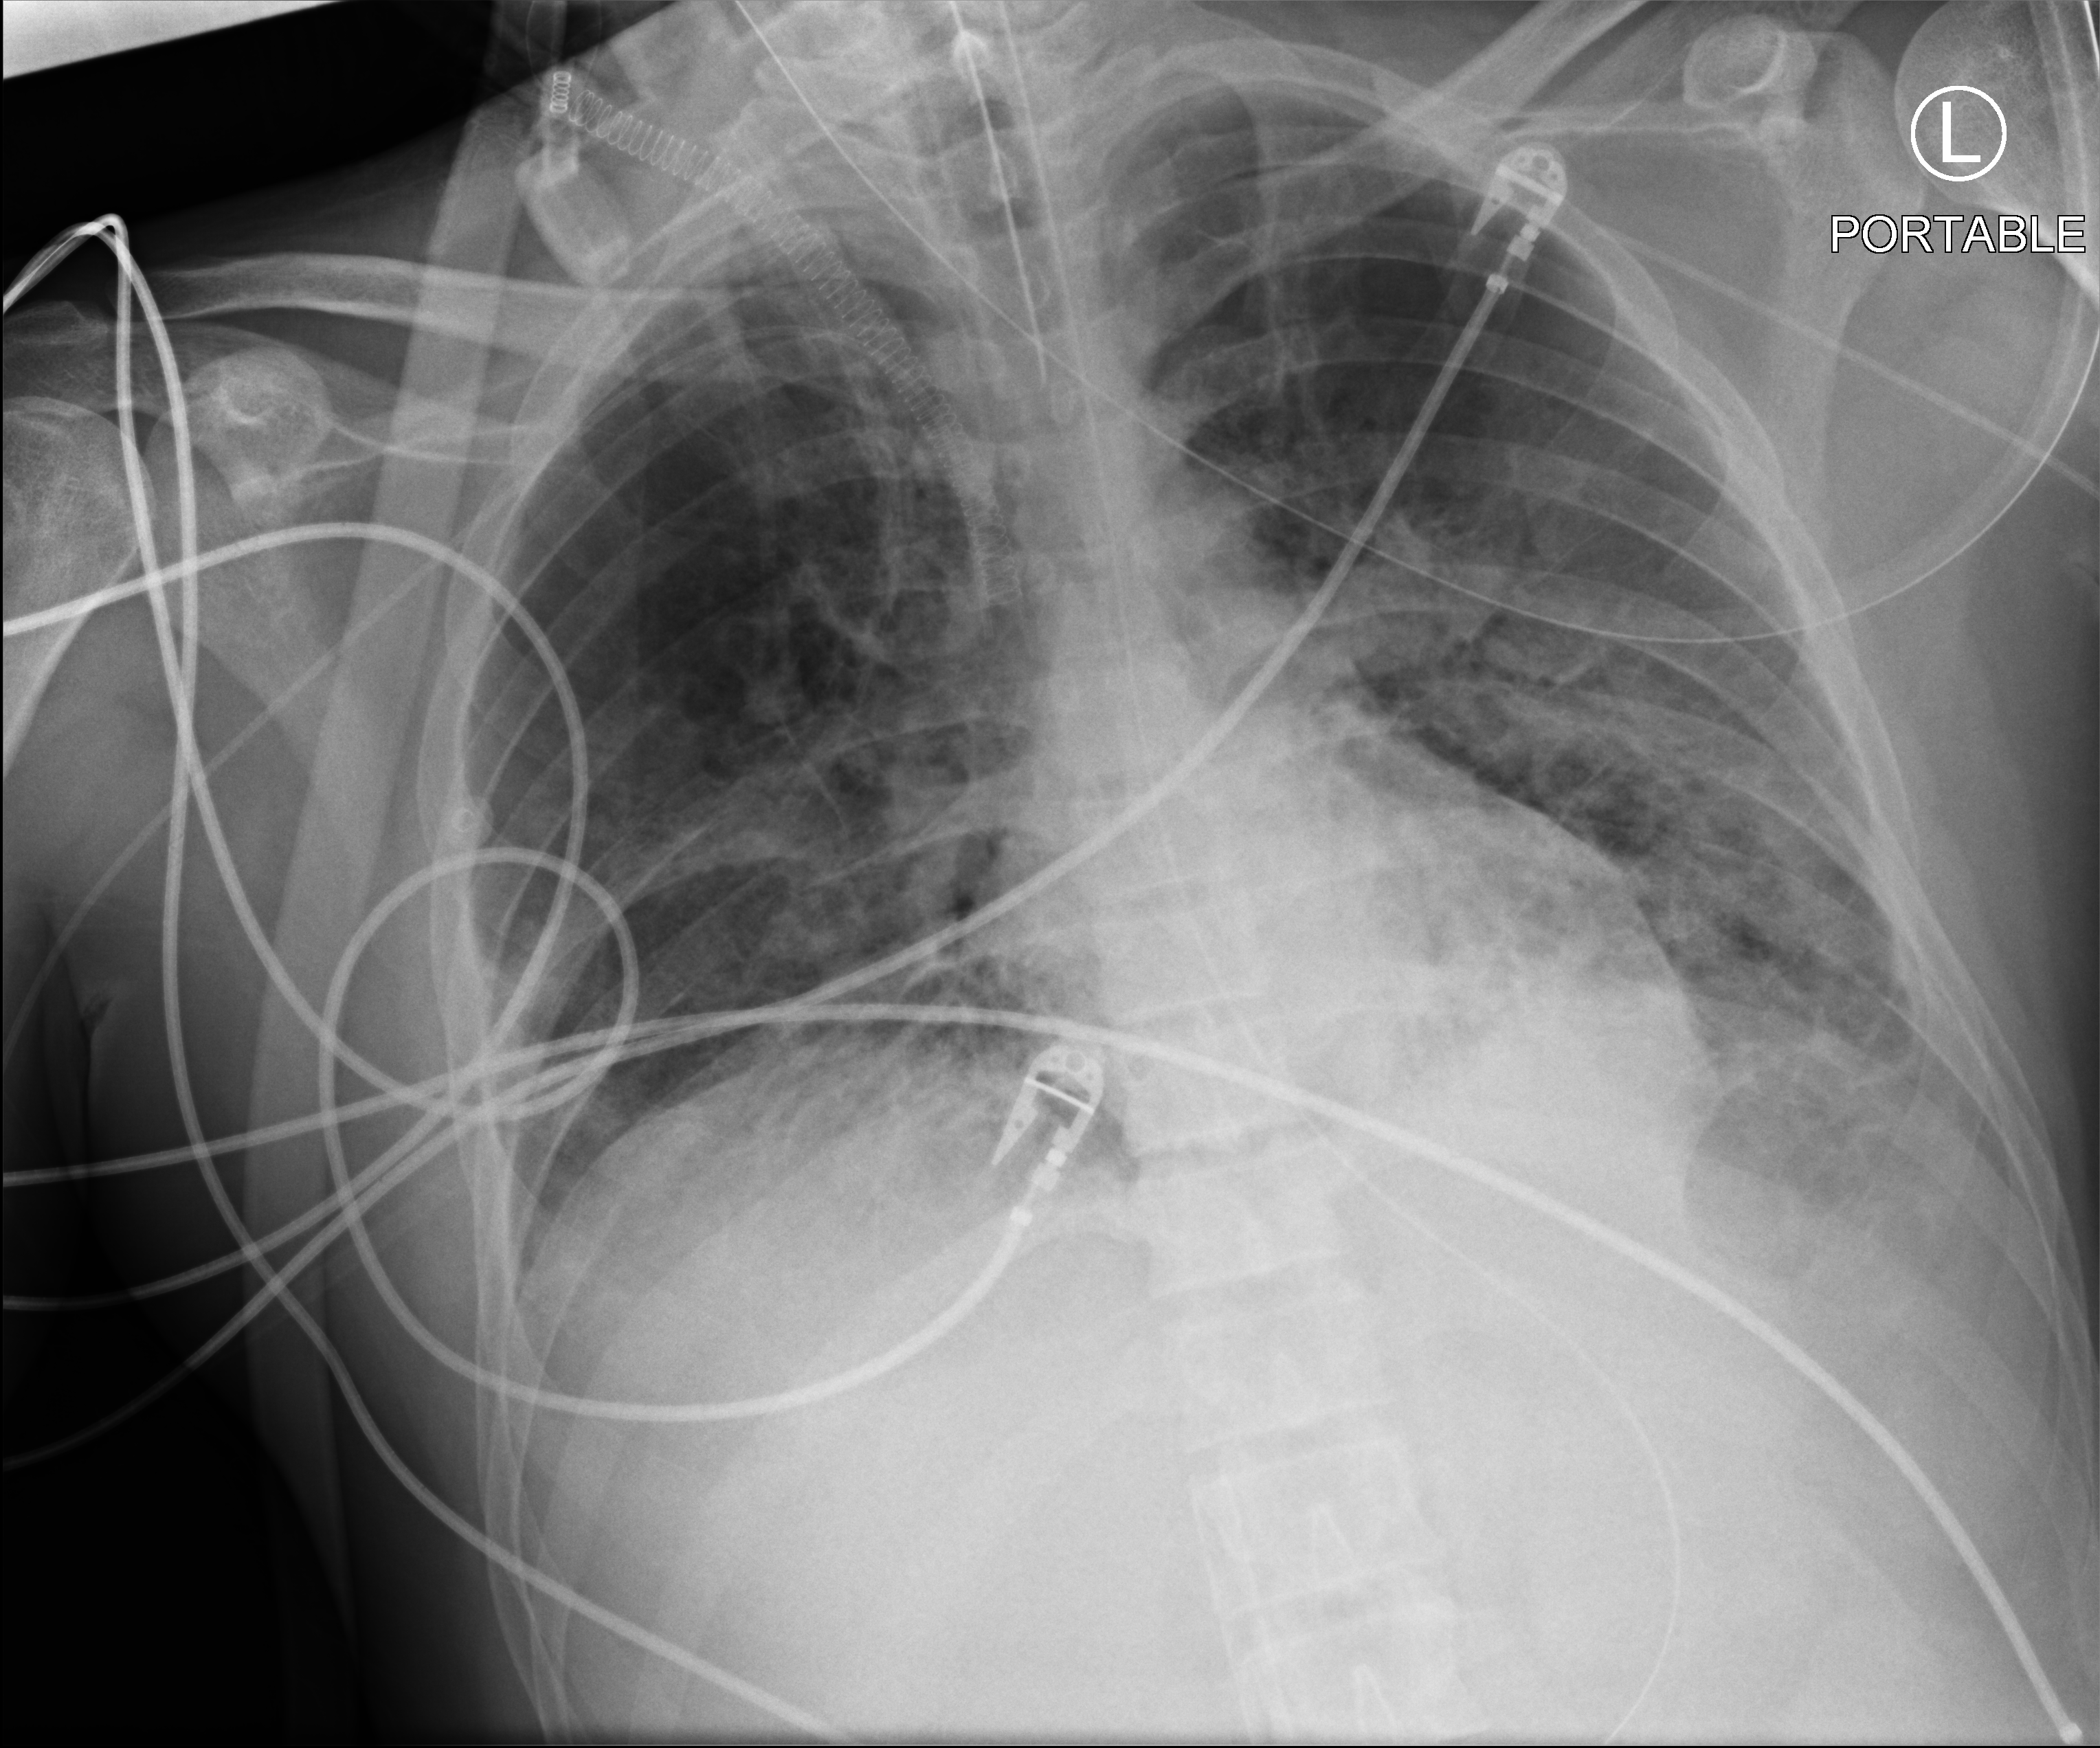
Chest X-ray (portable), anteroposterior (AP) projection. Adult patient hospitalised with COVID-19, age 18–59 years.
Admission-level facts for this patient (not findings on this image; timing relative to this image not recorded): mechanically ventilated during this hospital stay: yes.